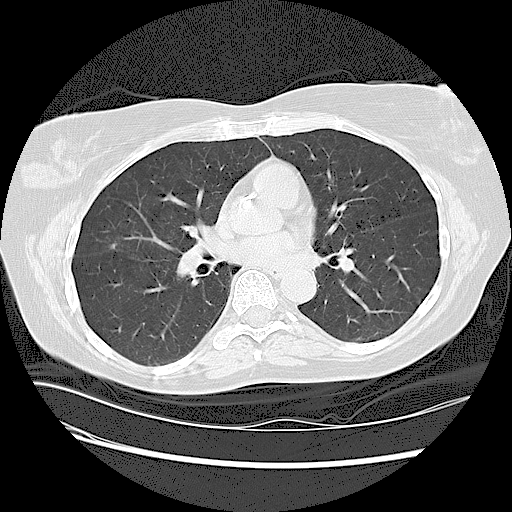
Low-dose screening chest CT, one axial slice. Slice 61 of 125 in the series (ordered by position). Reconstruction kernel LUNG. Lung window (W 1500 / L -600 HU). 2.5 mm slice thickness. 512 × 512 image matrix.
Annotated regions visible in this slice (outlined manually by an expert reader):
- lesion 1 (tumor, upper lobe of right lung): bounding box [x1, y1, x2, y2] px = [111, 244, 117, 249]